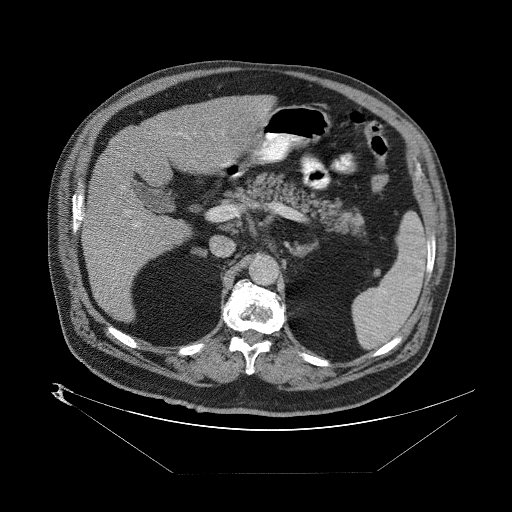
Contrast-enhanced abdominal CT (liver protocol), one axial slice. One of 2 acquisitions stored at this slice position. Soft-tissue window (W 400 / L 40 HU). 512 × 512 image matrix, field of view 480 × 480 mm. Case-level facts recorded for this patient, not image findings: diagnosis: hepatocellular carcinoma (patient treated with transarterial chemoembolisation; whether this scan precedes or follows treatment is not stated here); TNM stage (as recorded): Stage-II; Child-Pugh class: B; tumour differentiation: moderately differentiated; tumour nodularity: multinodular.
Outlined on this slice (semi-automatically segmented with operator editing):
- abdominal aorta: bounding box (x1, y1, x2, y2) in pixels: (250, 256, 277, 283)
- liver parenchyma outside the tumour (the mass and vessels are separate outlines, so this box may not span the whole liver): (82, 92, 270, 324)
- liver vessels: (114, 127, 224, 282)